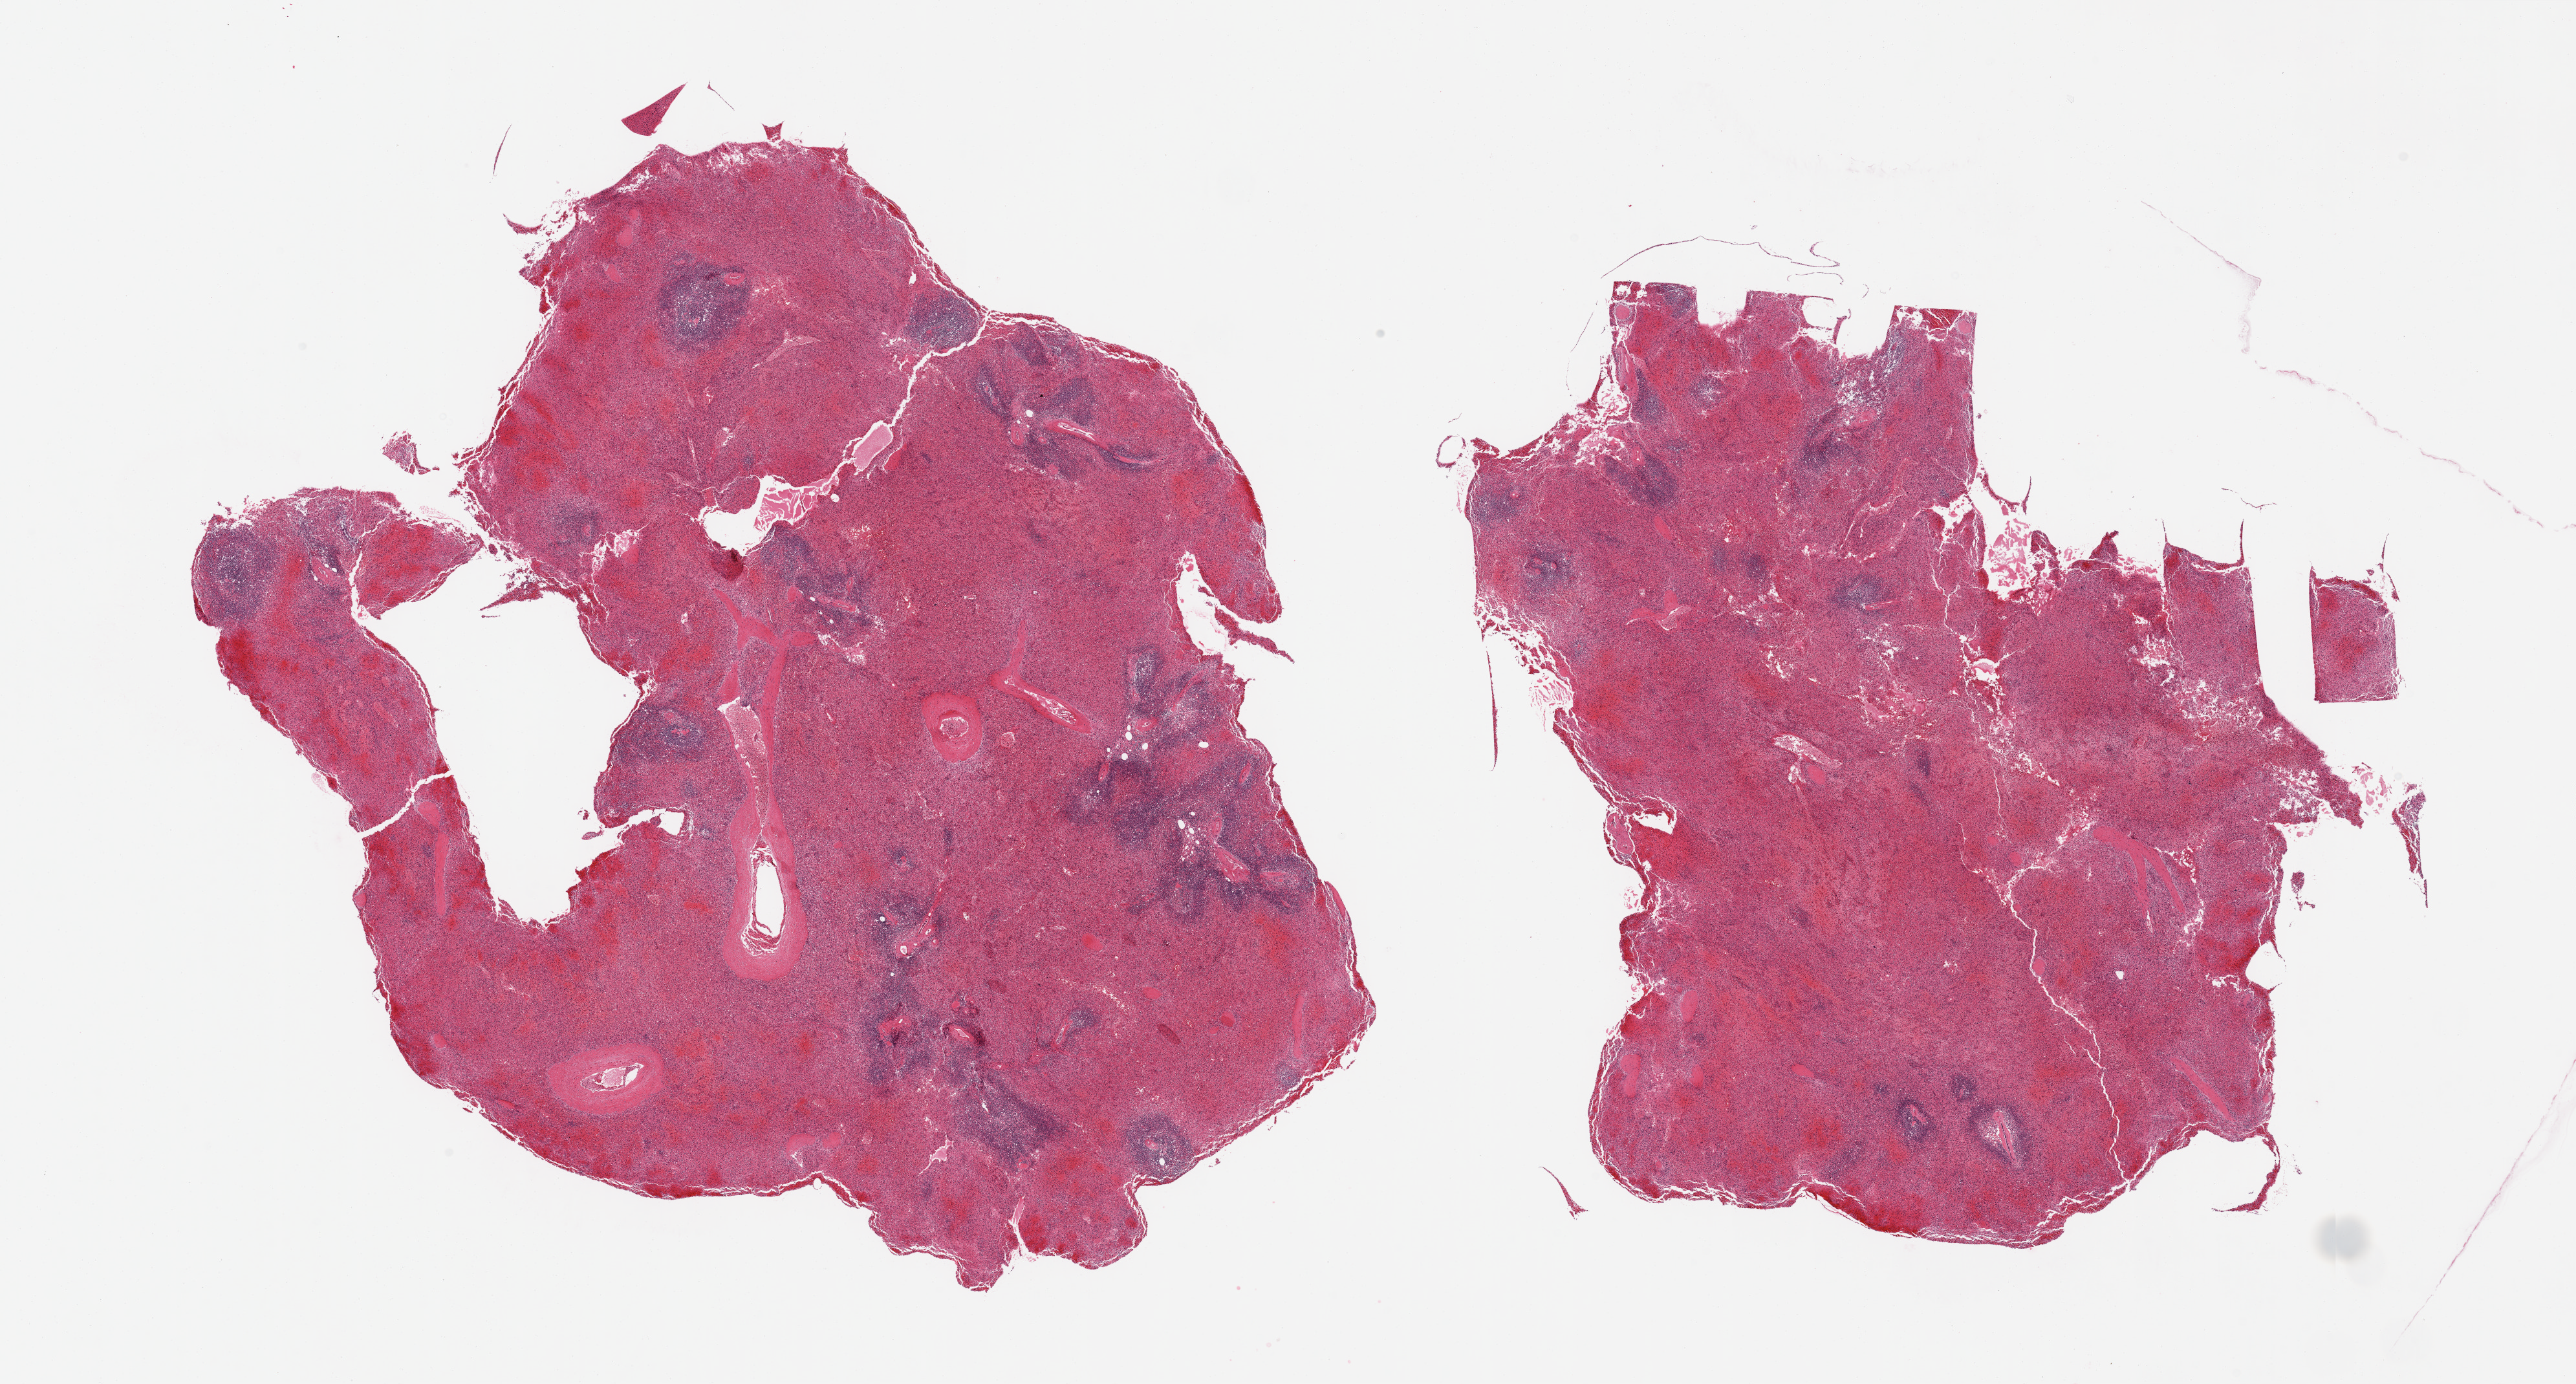
Whole-slide image, haematoxylin and eosin stain — whole scanned area (about 31.5 x 16.9 mm, from a 20x scan) shown as a low-resolution overview, PAXgene-fixed paraffin-embedded (PFPE) section, sampled site (target tissue): spleen, tissue donor sample. Donor: male.
Review note (as recorded): 2 pieces, moderate congestion.